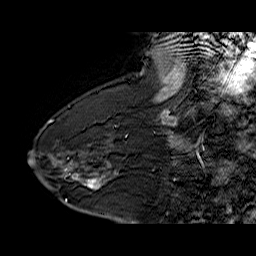
Breast MRI (dynamic contrast-enhanced), one sagittal slice. Dynamic contrast-enhanced series, time point 2 of 6 at this slice position (early post-contrast). 1.5 T. TE 6.4 ms, TR 32.9 ms. 256 × 256 image matrix, field of view 200 × 200 mm. Female patient. From the clinical record (not read from this slice): setting: breast cancer imaged before/during neoadjuvant chemotherapy; receptor status: HR-positive, HER2-negative.
Annotated regions visible in this slice (semi-automatically segmented with operator editing):
- analysis volume of interest (the breast-tissue region the enhancement analysis was run in; not a lesion): bounding box [x1, y1, x2, y2] px = [68, 154, 127, 201]
- tumour enhancement mask (voxels above the 100 % enhancement threshold inside the analysis volume of interest): [87, 179, 99, 189]